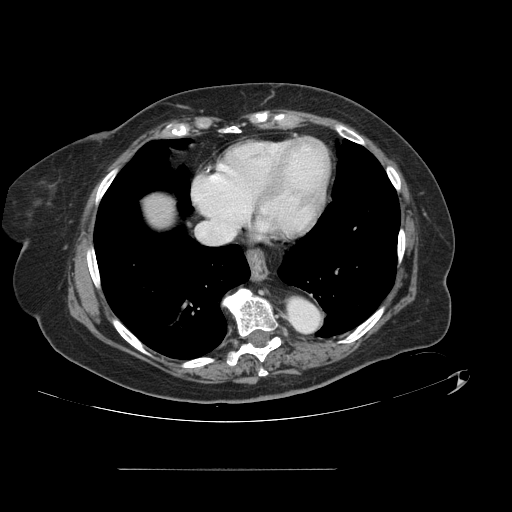
Contrast-enhanced abdominal CT, one axial slice. Position 131 of 148 along the scan axis. 120 kVp. Soft-tissue window (W 400 / L 40 HU). 2.5 mm slice thickness. 512 × 512 image matrix, field of view 439 × 439 mm. Female patient, age 75 years. Case-level facts recorded for this patient, not image findings: diagnosis: colorectal cancer liver metastases, imaged before liver resection; multiple liver metastases: no; largest metastasis: 2.4 cm.
Outlined on this slice (outlined manually by an expert reader):
- liver: box from (x=143, y=194) to (x=177, y=227) px
- planned liver remnant (the part of the liver to remain after resection): (x=143, y=195)–(x=174, y=228)